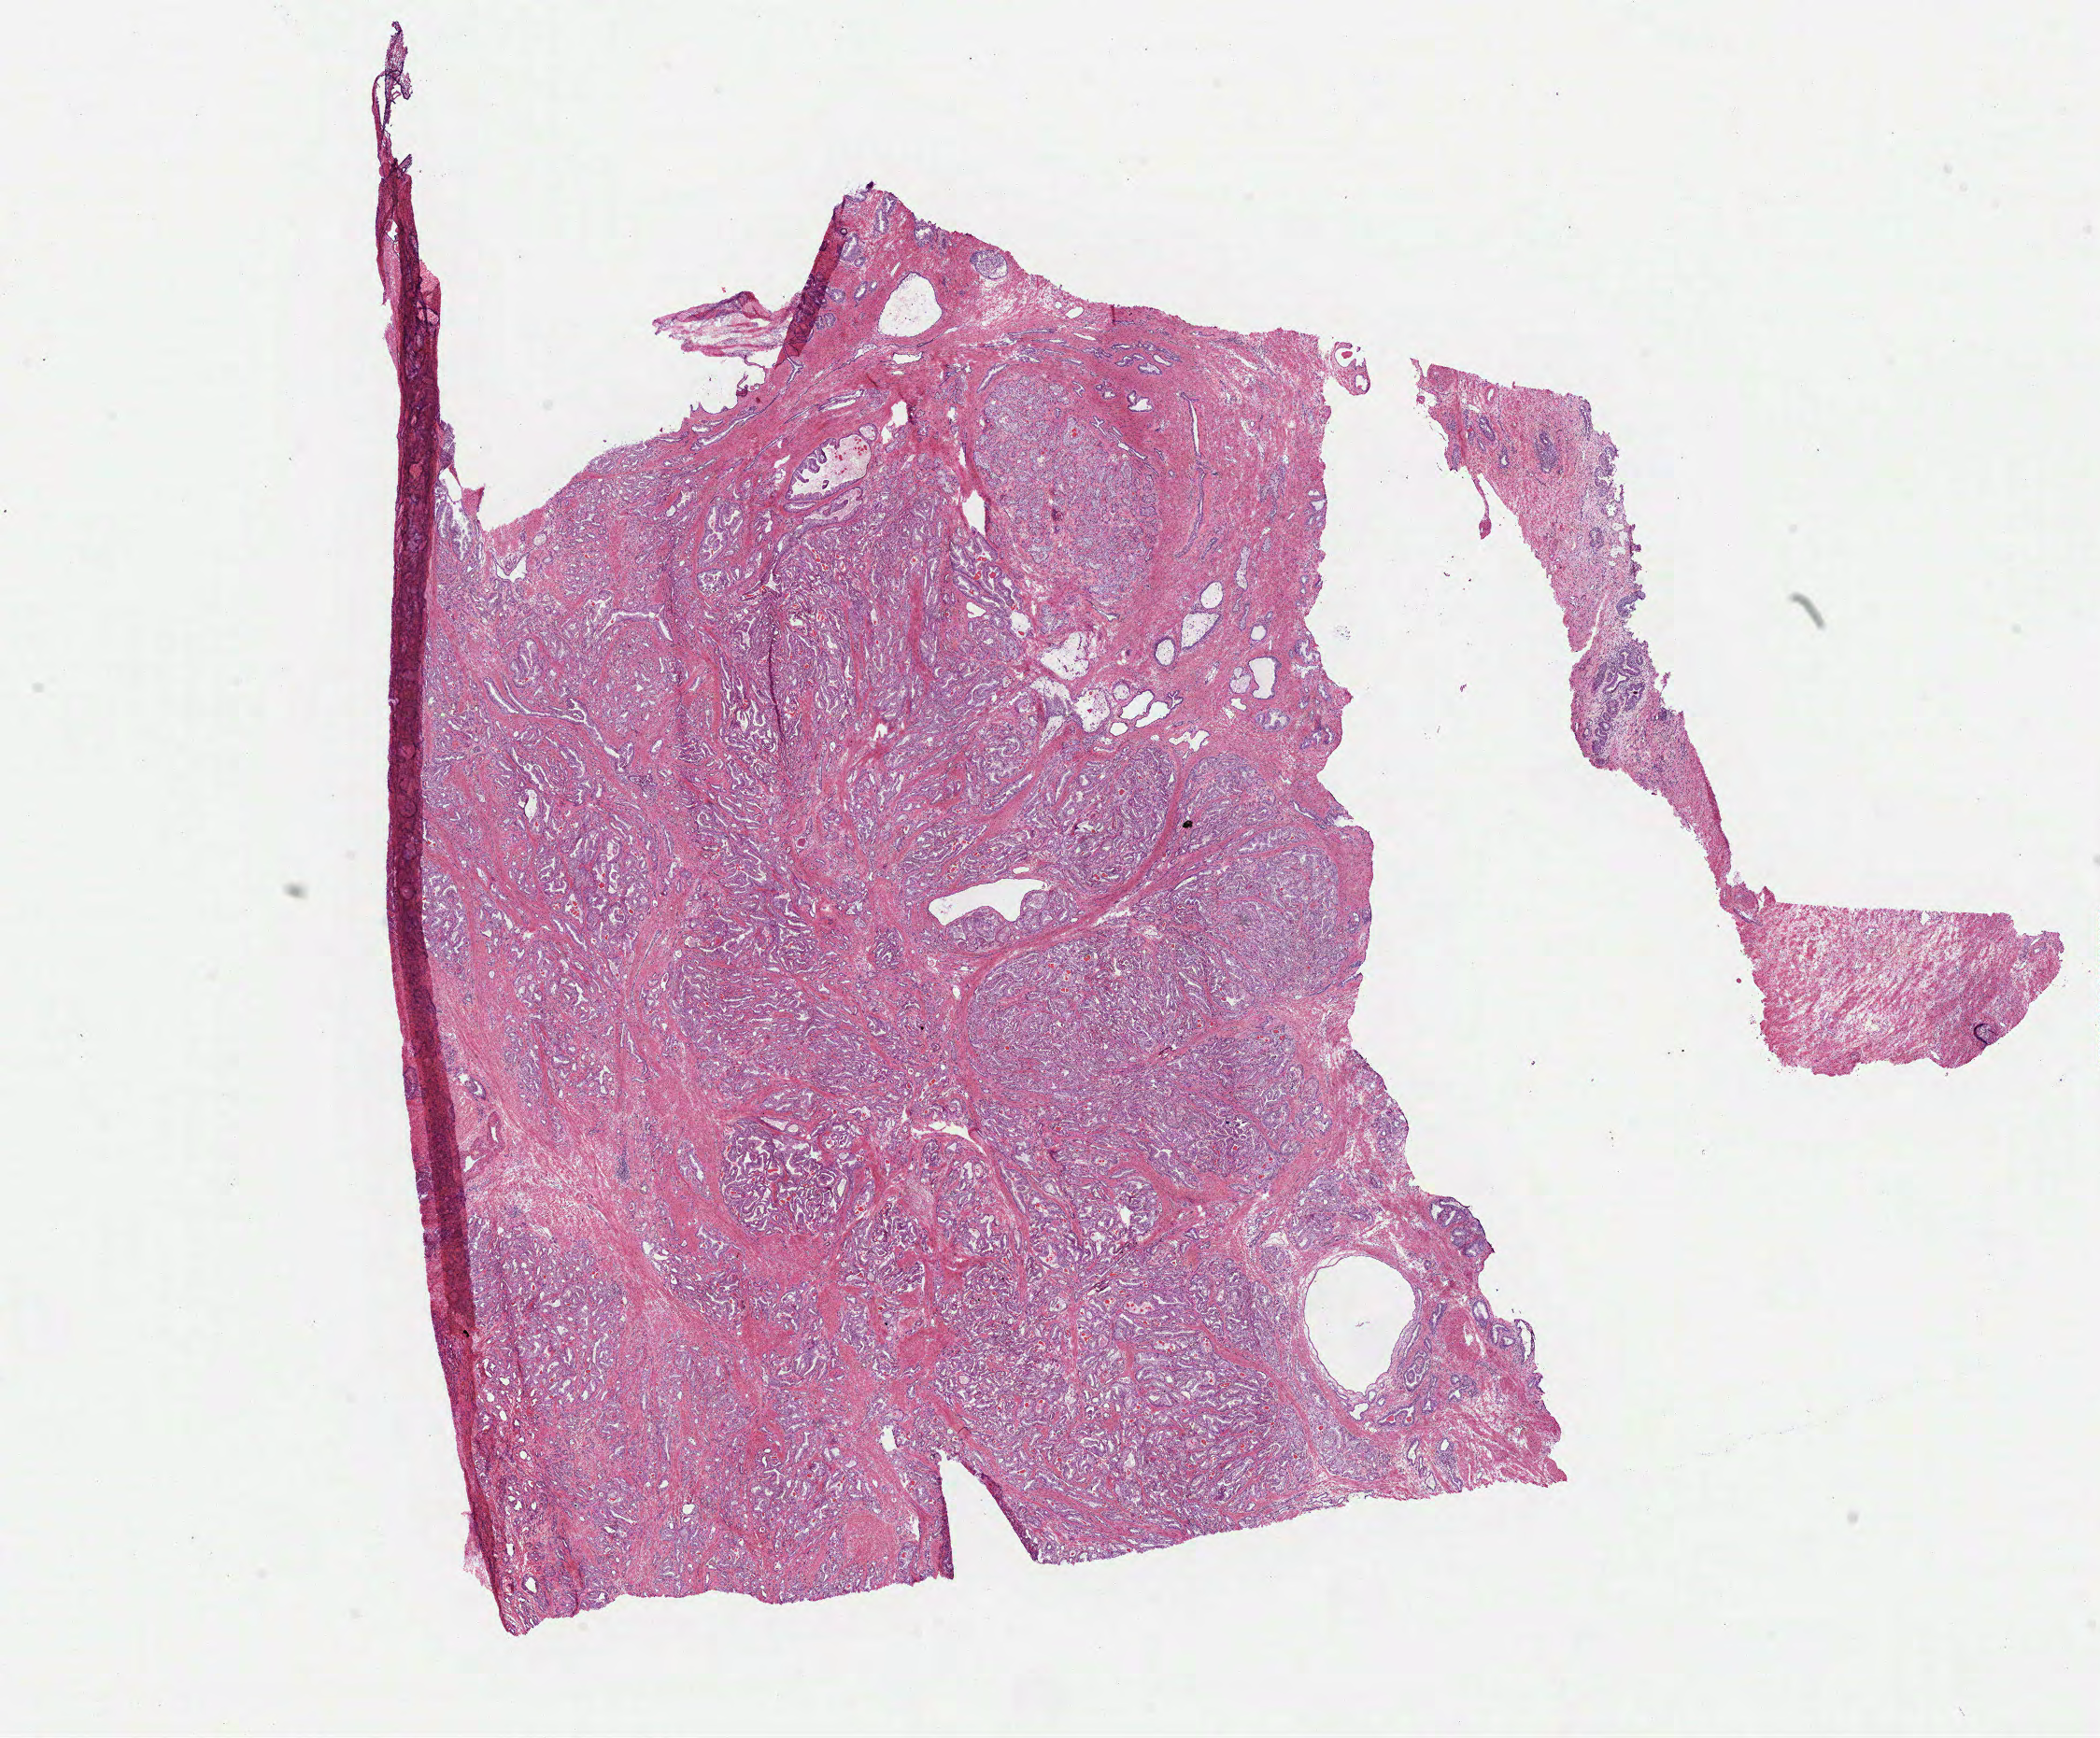
Whole-slide histology image, H&E-stained — whole scanned area (about 18.1 x 15.0 mm, slide scanned at 40x) shown as a low-resolution overview; frozen section from the bottom of the tissue portion; prostate, primary tumour sample. Male patient; age at initial diagnosis 67 years. Gleason score: 7 (3+4). Pathologist review of this section (percent, as recorded): tumour cells 80%, tumour nuclei 90%, normal cells 5%, stromal cells 15%, necrosis 0%. Inflammatory infiltration, as recorded: lymphocyte infiltration 0%, monocyte infiltration 0%, neutrophil infiltration 0%.
Histologic diagnosis: Acinar cell carcinoma (prostate gland).